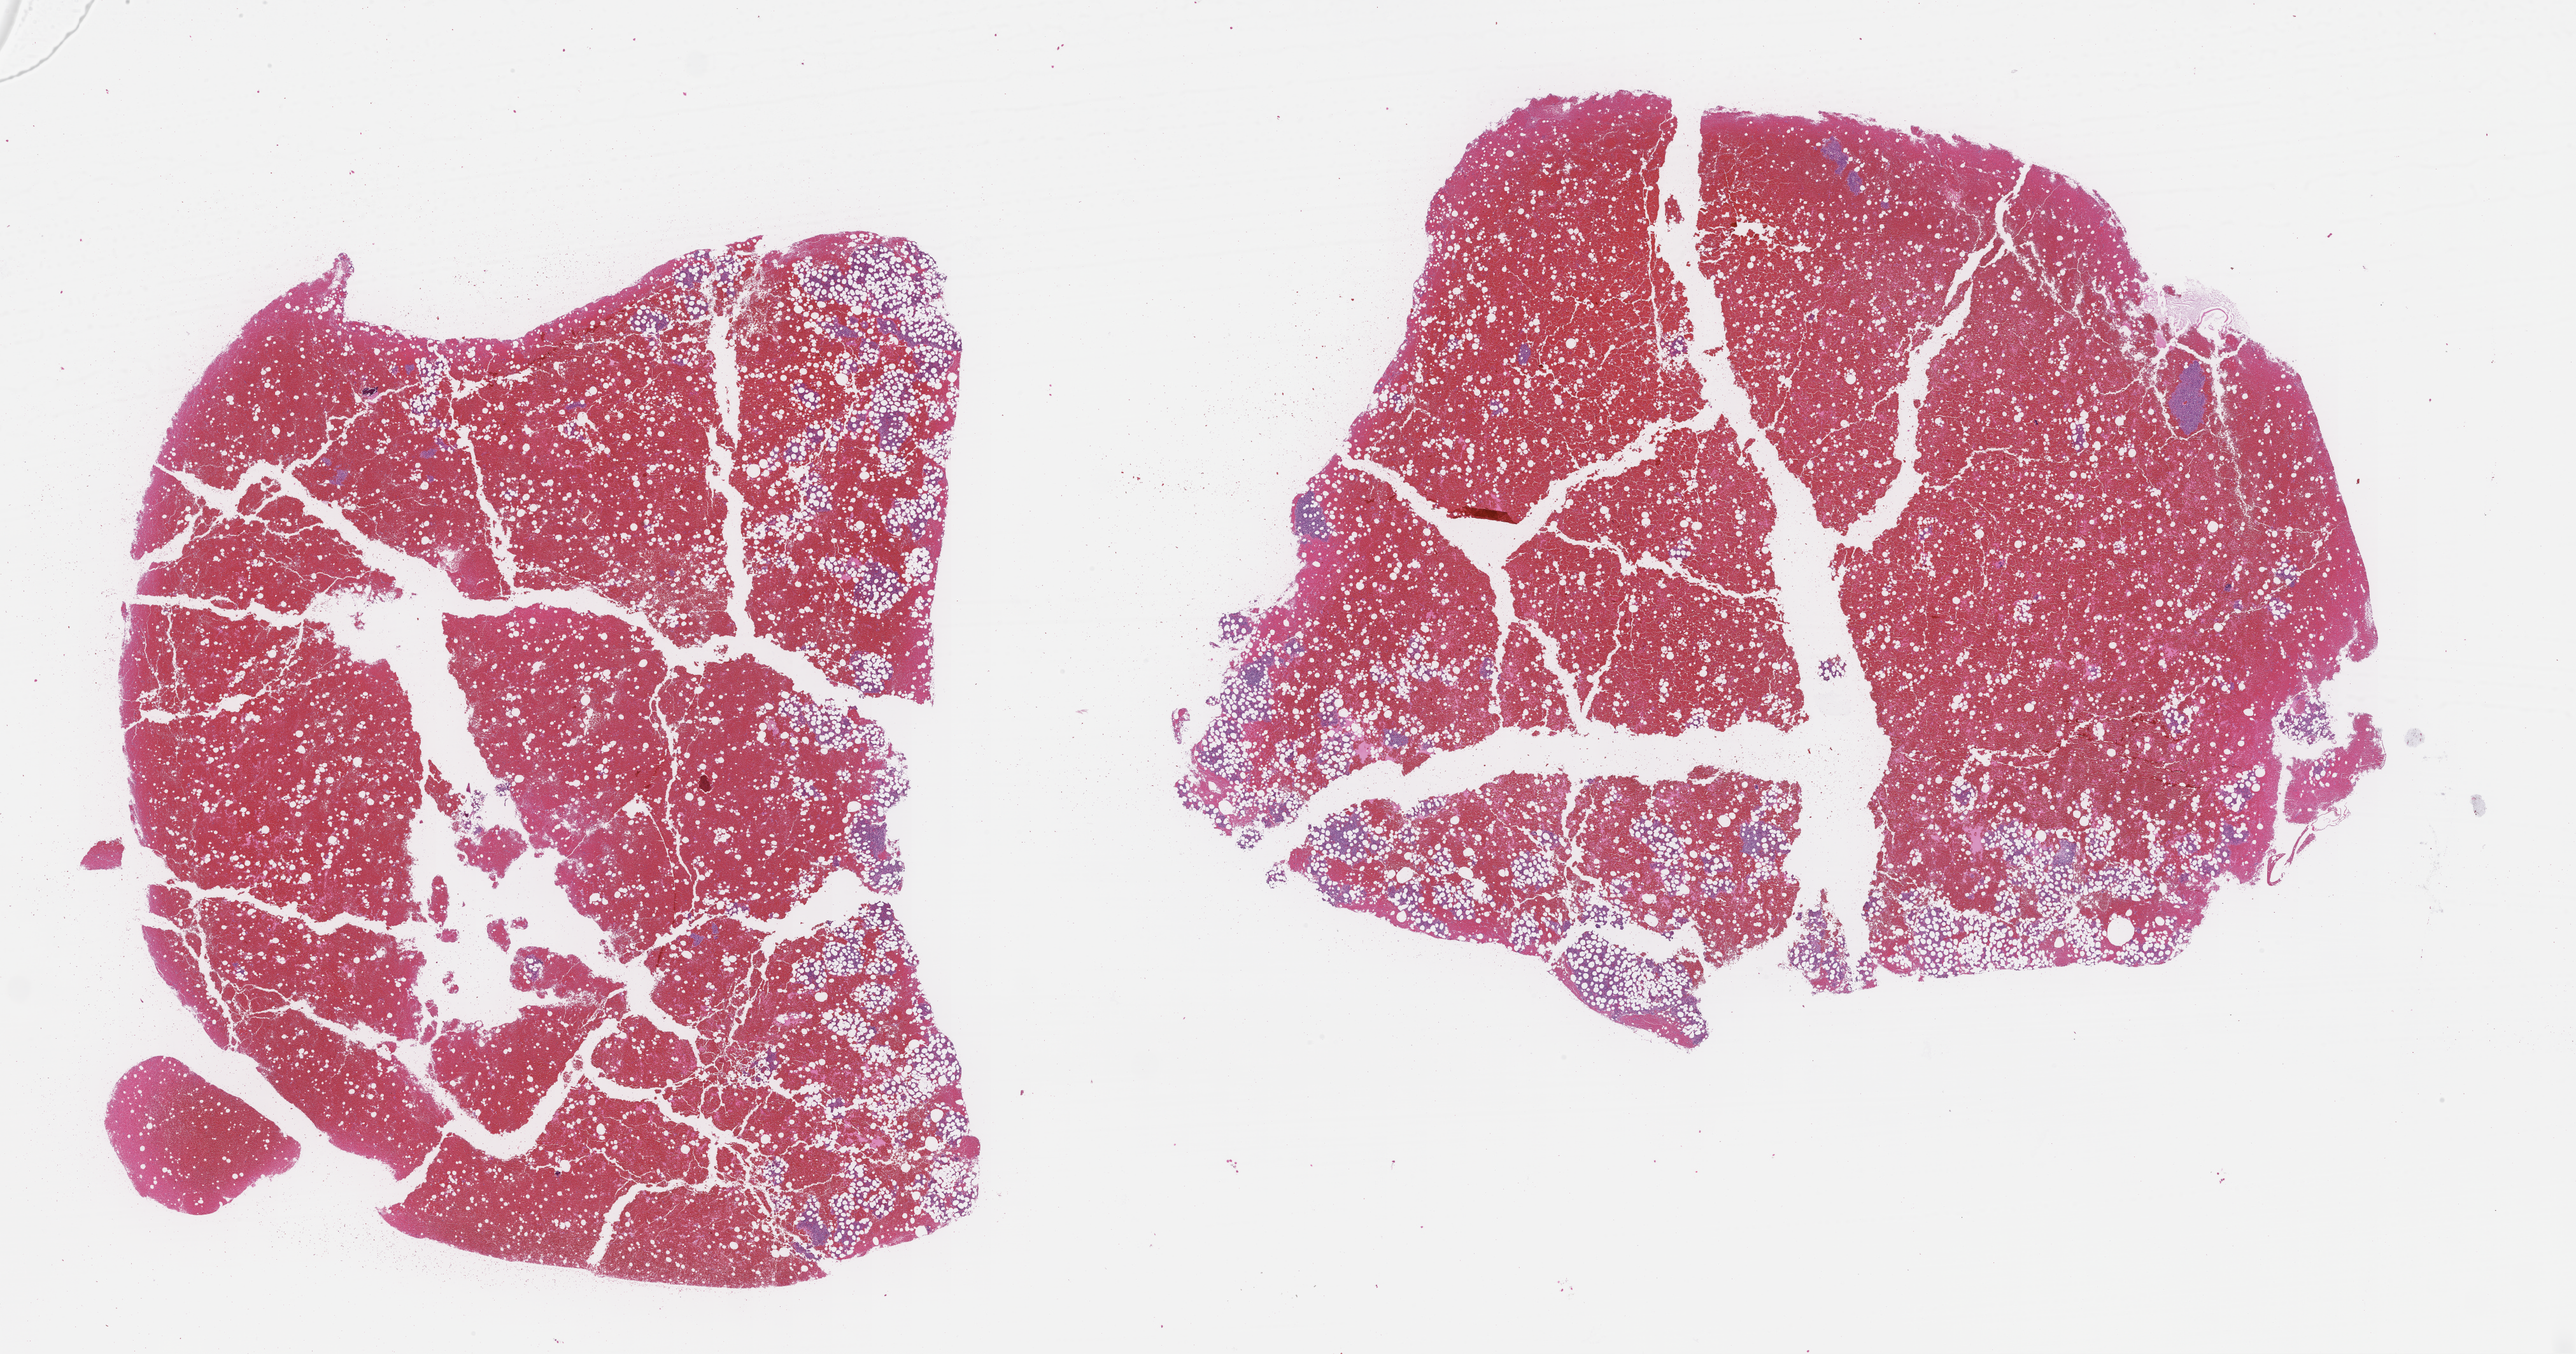
Digitized haematoxylin and eosin-stained section — a low-resolution overview of the entire scanned area, about 32.7 x 17.2 mm. FFPE section. Site: bone marrow. Collected on treatment. Patient: male.
Patient diagnosis: Plasma Cell Myeloma.